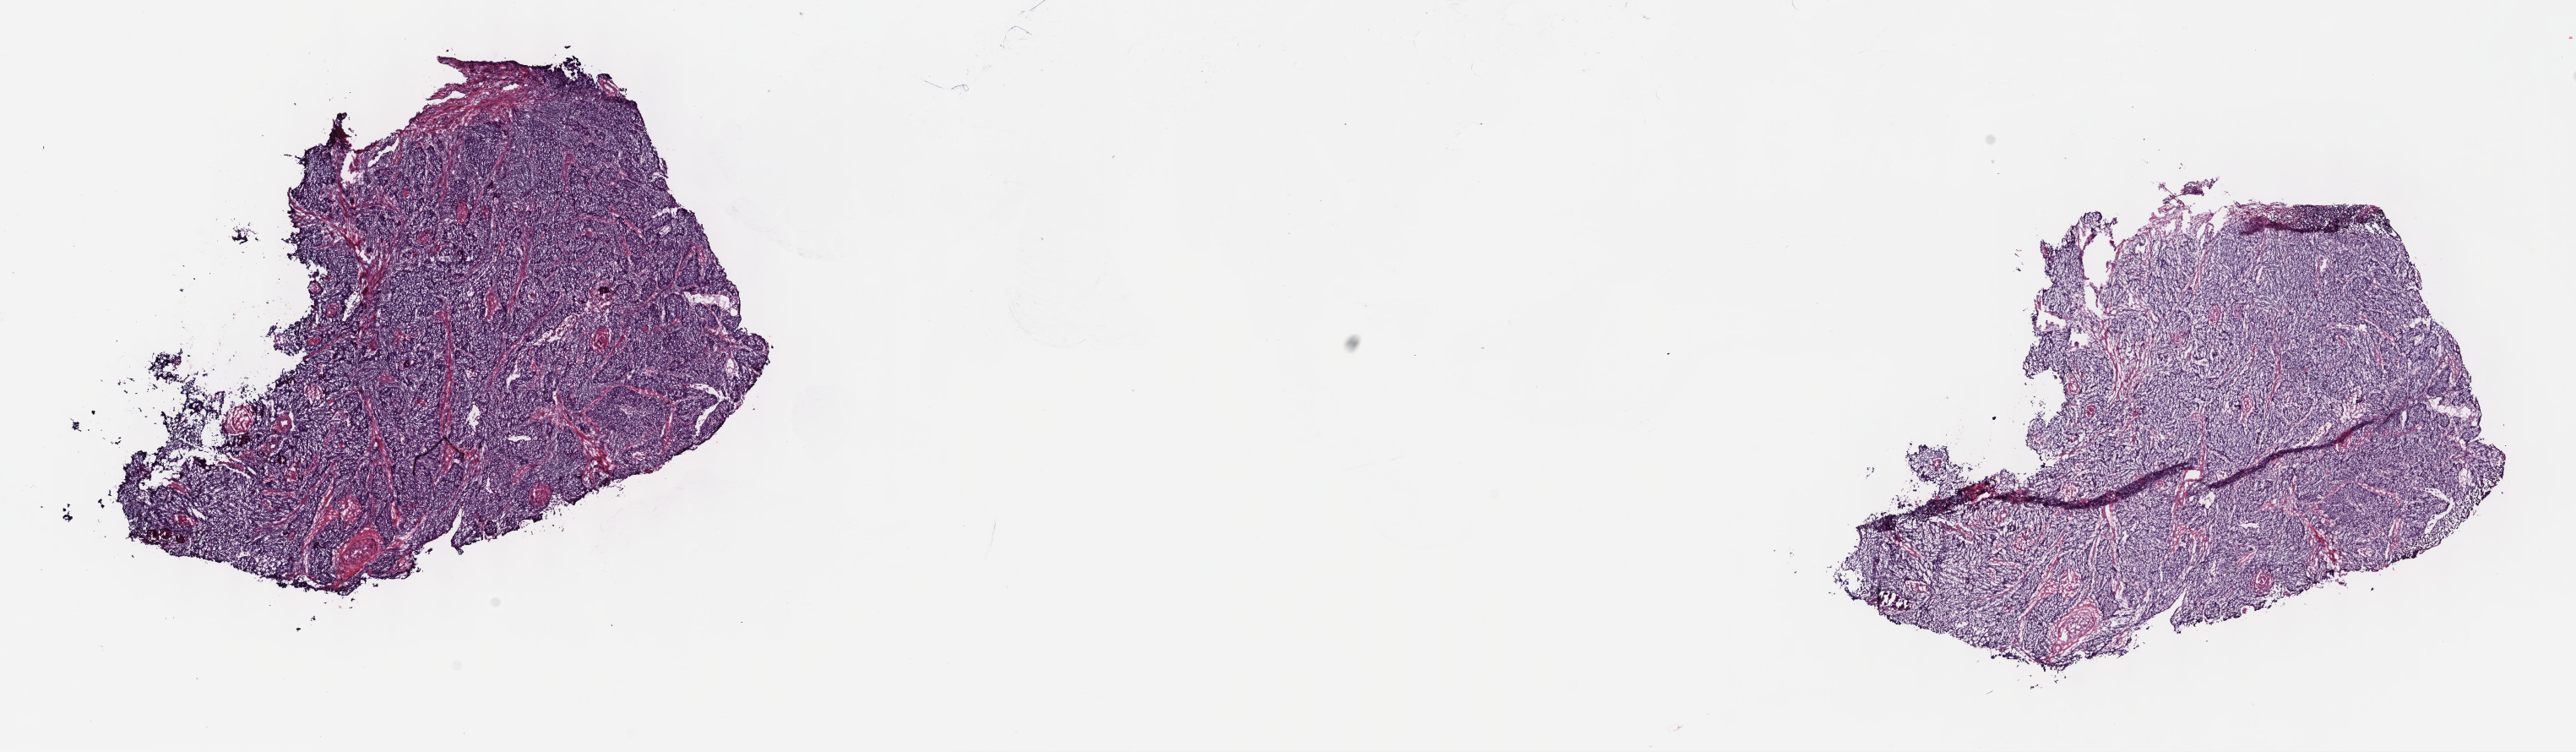
H&E whole-slide image — a low-resolution overview of the entire scanned area, about 24.7 x 7.2 mm (slide scanned at 40x), frozen section from the top of the tissue portion, primary tumour sample from the cervix. Female, age 55 years at initial diagnosis. Histologic grade: G2 (moderately differentiated). Composition of this section per pathologist review: tumour cells 97%, tumour nuclei 75%, normal cells 0%, stromal cells 0%, necrosis 3%. Infiltration values recorded for this section: lymphocyte infiltration 4%, monocyte infiltration 0%, neutrophil infiltration 0%.
Lymph nodes positive (case pathology): 0 of 47 examined. Diagnosis: Squamous cell carcinoma, NOS (cervix uteri). FIGO stage: IB.